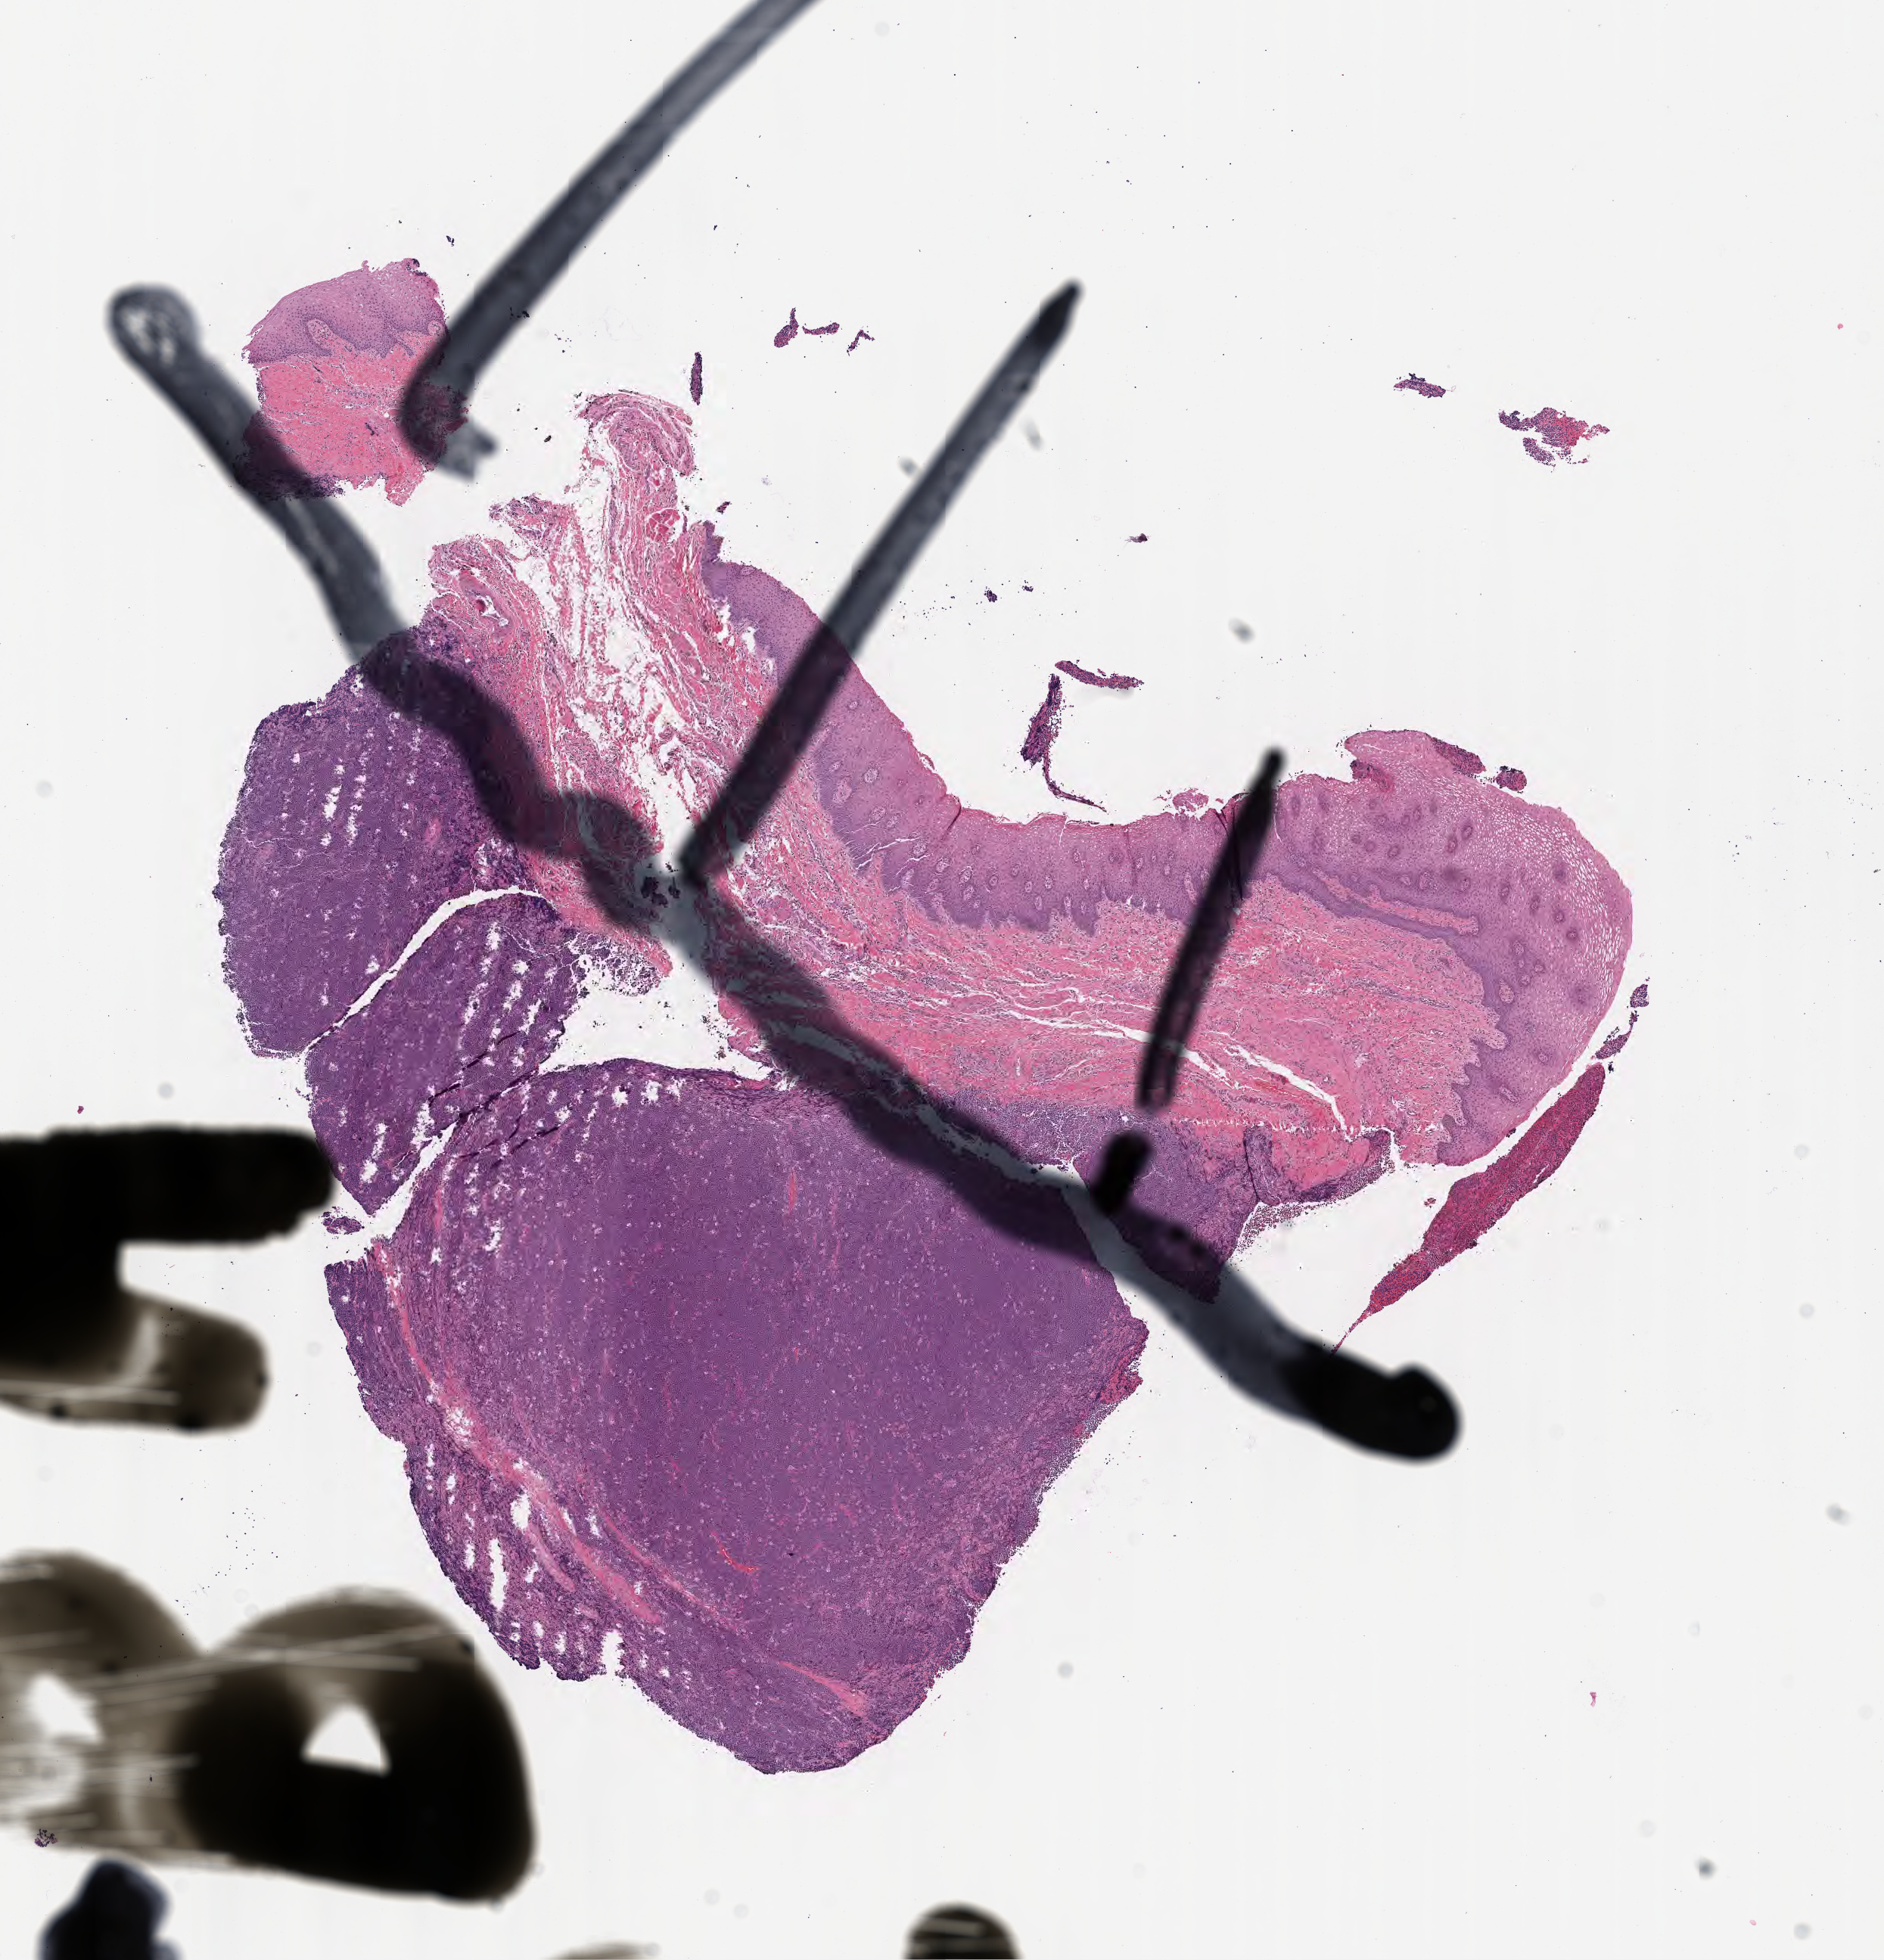
Whole-slide image, haematoxylin and eosin stain — whole scanned area (about 10.1 x 10.5 mm) shown as a low-resolution overview, specimen: tumor tissue, site: mandible. Female patient, aged 13.
Diagnosis: Burkitt lymphoma, NOS.